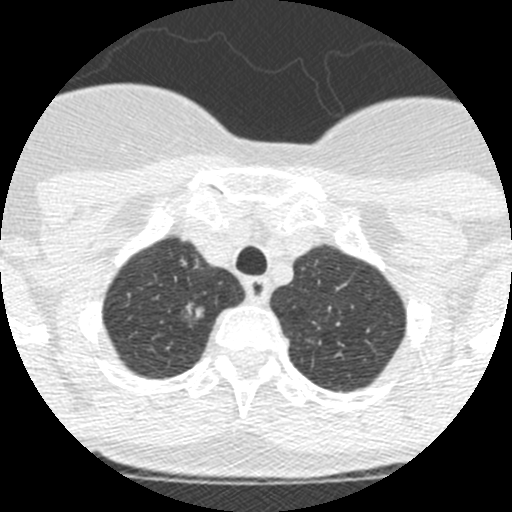
Low-dose screening chest CT, one axial slice. Slice 212 of 250 in the series (ordered by position). 120 kVp. Lung window (W 1500 / L -600 HU). 1.25 mm slice thickness. 512 × 512 image matrix, field of view 257 × 257 mm.
Annotated regions visible in this slice (expert manual segmentation):
- lesion 1 (tumor, upper lobe of right lung): bounding box <186,303,204,318> (left, top, right, bottom; pixels)